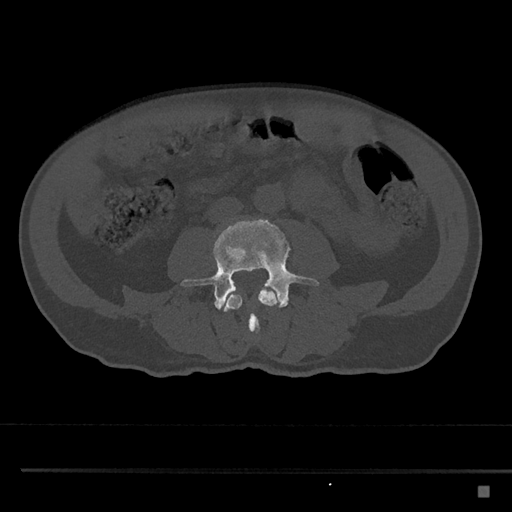
CT including the spine, one axial slice. Slice 656 of 797 in the series (ordered by position). Reconstruction kernel Br40s/3. Bone window (W 1800 / L 400 HU). 0.5 mm slice thickness. 512 × 512 image matrix, field of view 391 × 391 mm. Patient: male, 59 years. Case-level facts recorded for this patient, not image findings: primary cancer: prostate.
Outlined on this slice (semi-automatically segmented with operator editing):
- L3 vertebra: bounding box (x1, y1, x2, y2) in pixels: (219, 286, 278, 333)
- L4 vertebra: (181, 218, 320, 309)